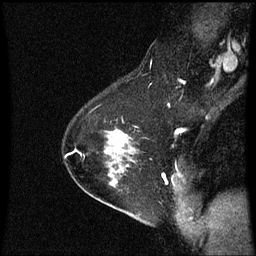
Breast MRI (dynamic contrast-enhanced), one sagittal slice. Position 43 of 60 along the scan axis. Dynamic contrast-enhanced series, image 2 of 3 at this slice position (ordered by acquisition). 1.5 T. TE 4.2 ms, TR 8.9 ms. 256 × 256 image matrix, field of view 200 × 200 mm. Patient: female, 54 years. Case-level facts recorded for this patient, not image findings: setting: breast cancer imaged before/during neoadjuvant chemotherapy; receptor status: HER2-positive.
Annotated regions visible in this slice (semi-automatically segmented with operator editing):
- analysis volume of interest (the breast-tissue region the enhancement analysis was run in; not a lesion): bounding box <104,128,137,169> (left, top, right, bottom; pixels)
- tumour enhancement mask (voxels above the 70 % enhancement threshold inside the analysis volume of interest): <113,130,128,147>